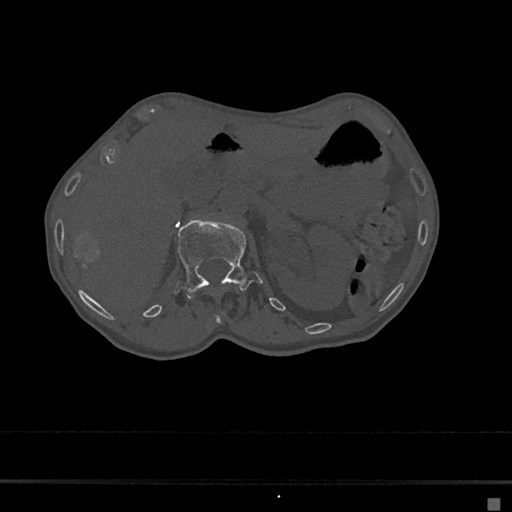
CT including the spine, one axial slice; slice 76 of 797 in the series (ordered by position); bone window (W 1800 / L 400 HU); 0.5 mm slice thickness; 512 × 512 image matrix, field of view 360 × 360 mm. Patient: female, 68 years. From the clinical record (not read from this slice): primary cancer: renal.
Outlined on this slice (semi-automatically segmented with operator editing):
- L1 vertebra: bounding box (x1, y1, x2, y2) in pixels: (174, 217, 262, 298)
- T12 vertebra: (213, 313, 223, 325)